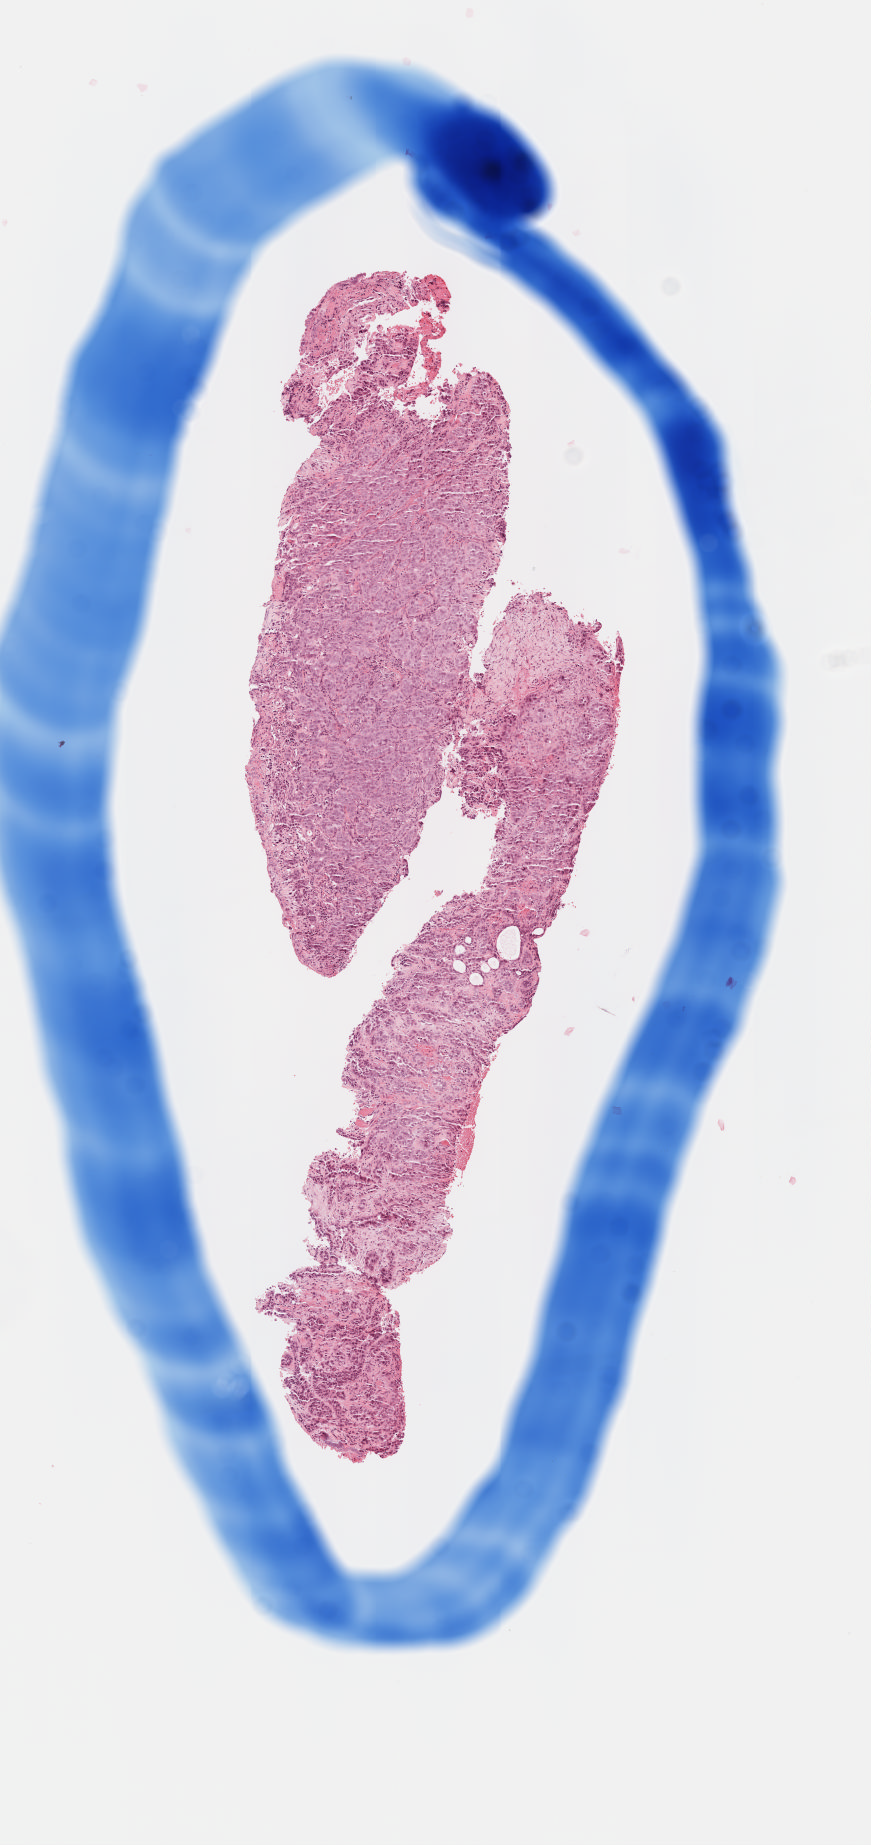
Digitized H&E-stained tissue section (whole slide), low-resolution overview of the scanned area, about 3.5 x 7.5 mm (slide scanned at 40x); formalin-fixed paraffin-embedded (FFPE) diagnostic section; sample: primary tumour, head and neck. Male patient; age at initial diagnosis 52 years. Histologic grade: G3 (poorly differentiated).
Diagnosis: Squamous cell carcinoma, NOS (tongue, NOS).